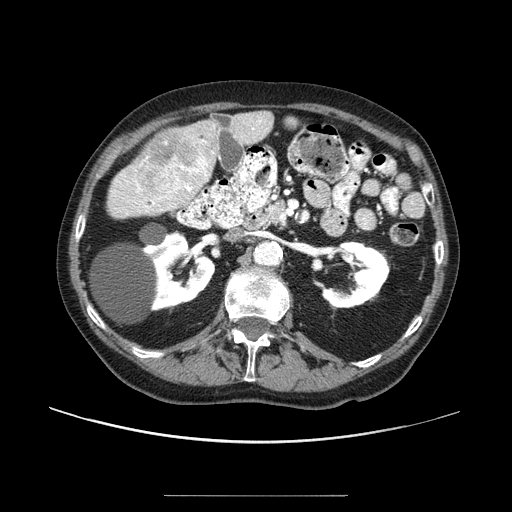
Contrast-enhanced abdominal CT (liver protocol), one axial slice; slice 37 of 91 in the series (ordered by position); reconstruction kernel STANDARD; 100 kVp; one of 2 acquisitions stored at this slice position; soft-tissue window (W 400 / L 40 HU); 2.5 mm slice thickness; 512 × 512 image matrix, field of view 400 × 400 mm. Case-level facts recorded for this patient, not image findings: diagnosis: hepatocellular carcinoma (patient treated with transarterial chemoembolisation; whether this scan precedes or follows treatment is not stated here); TNM stage (as recorded): Stage-I; Child-Pugh class: A; tumour differentiation: moderately differentiated; tumour nodularity: uninodular.
Annotated regions visible in this slice (semi-automatically segmented with operator editing):
- liver parenchyma outside the tumour (the mass and vessels are separate outlines, so this box may not span the whole liver): bounding box <171,110,272,202> (left, top, right, bottom; pixels)
- mass: <132,129,211,200>
- liver vessels: <201,120,261,153>